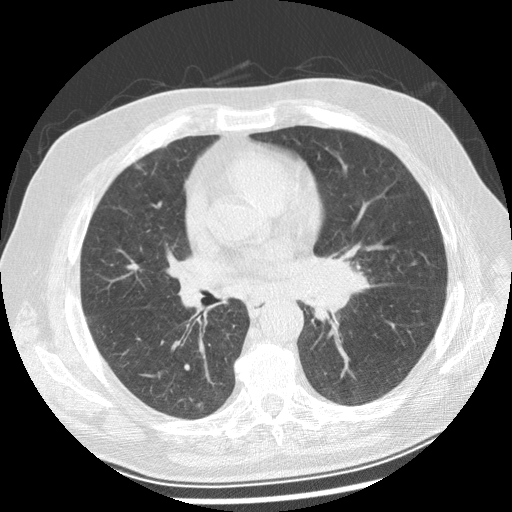
Chest CT (low-dose screening protocol), one axial image, baseline annual screen, lung window (W 1500 / L -600 HU), 2.5 mm slice thickness, standard (soft-tissue) reconstruction kernel (STANDARD), 512 × 512 image matrix. Male participant, aged 70 years at enrolment. Current smoker at enrolment.
• Lesion marked by an expert reader, bounding box (x1, y1, x2, y2) in pixels: (289, 241, 372, 320).
• Screening reader's record for this exam: no non-calcified nodule ≥4 mm recorded.
• Lung cancer was diagnosed 29 days after this screen: squamous cell carcinoma, keratinizing, NOS, left main stem bronchus, moderately differentiated (G2), stage IIIB (AJCC 6th edition), 40 mm at pathology.